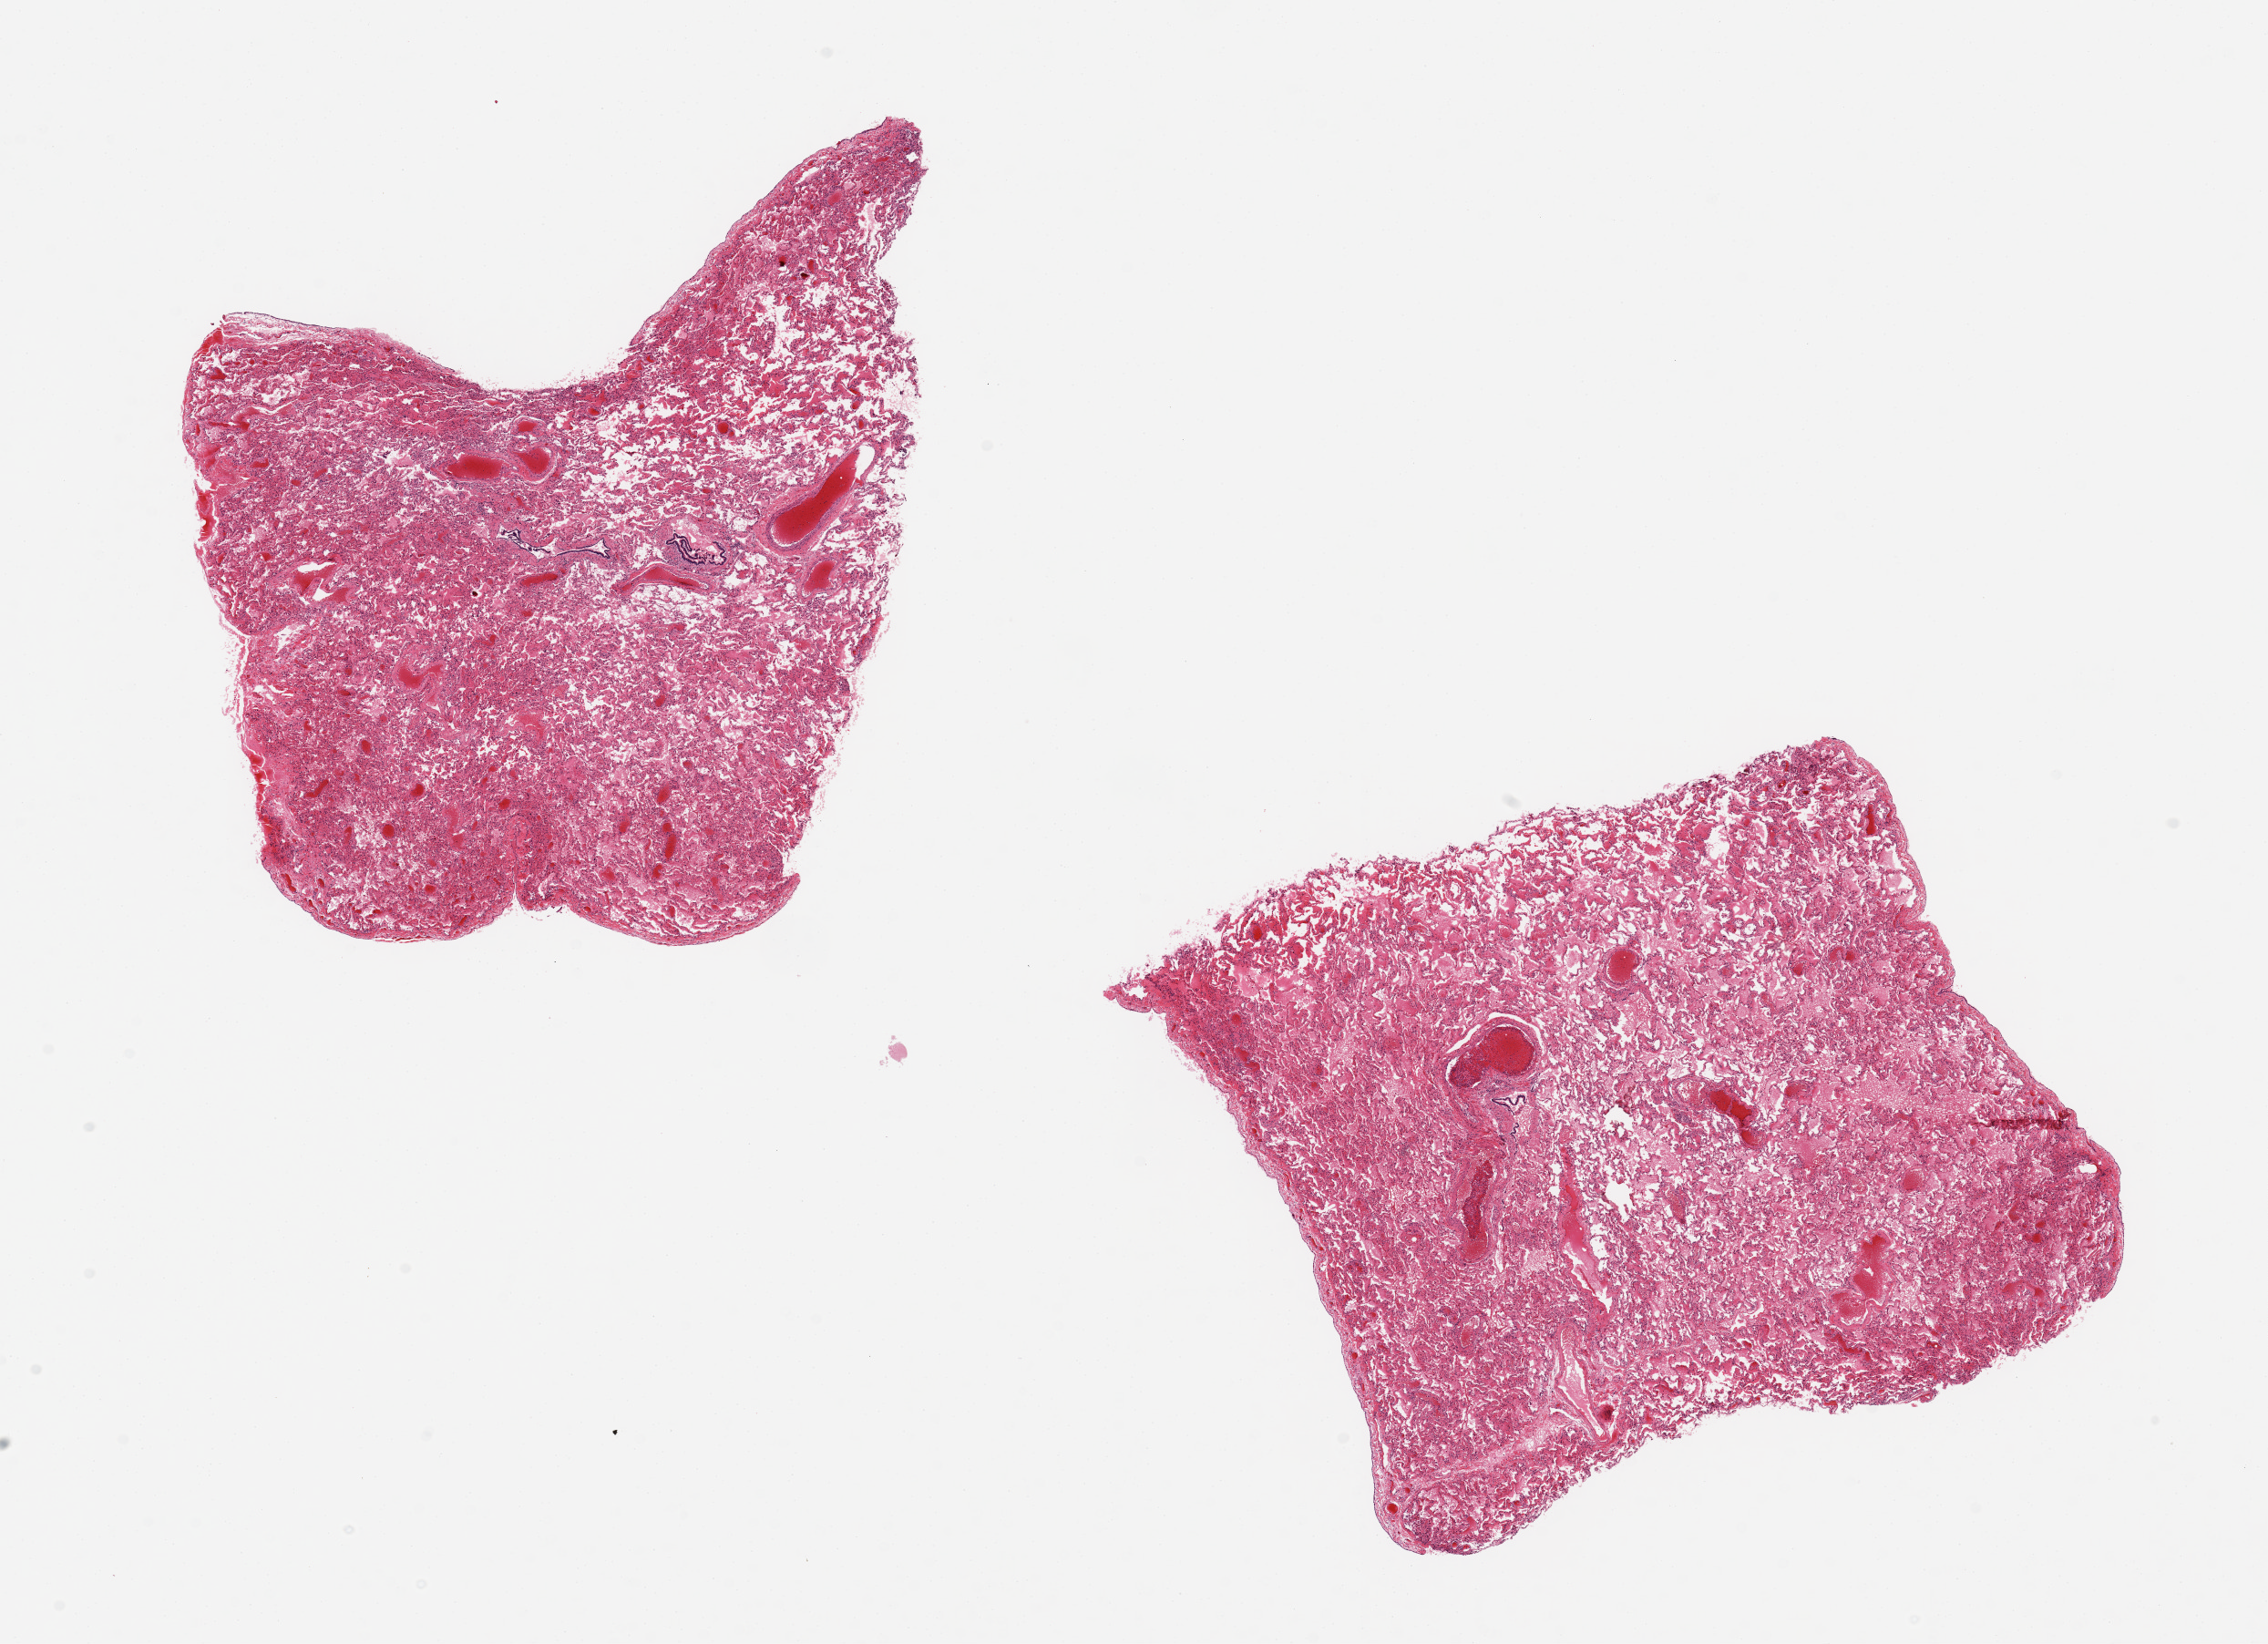
Whole-slide image, haematoxylin and eosin stain, shown as a low-resolution overview of the whole scanned area (about 19.7 x 14.3 mm), PAXgene-fixed, paraffin-embedded tissue, section of lung (target tissue), donor tissue sample. Donor sex: male.
Reviewer comment on this tissue sample: 2 pieces 7x6 & 7x5 mm; moderate venous congestion; moderate alveolar fluid; no pneumonia.